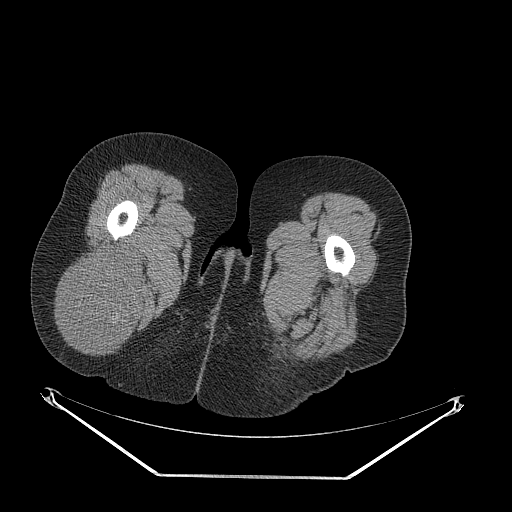
CT of an extremity soft-tissue mass (from a PET/CT study), one axial slice. Position 44 of 257 along the scan axis. 140 kVp. Soft-tissue window (W 400 / L 40 HU). 3.75 mm slice thickness. 512 × 512 image matrix, field of view 500 × 500 mm. Female patient. From the clinical record (not read from this slice): histological type: synovial sarcoma; grade: intermediate; site of the primary tumour: right buttock.
Annotated regions visible in this slice (expert contour drawn on MRI and transferred to this co-registered scan by the dataset authors):
- gross tumour volume including surrounding oedema: box from (x=62, y=247) to (x=147, y=348) px
- gross tumour volume (mass): (x=62, y=247)–(x=147, y=348)